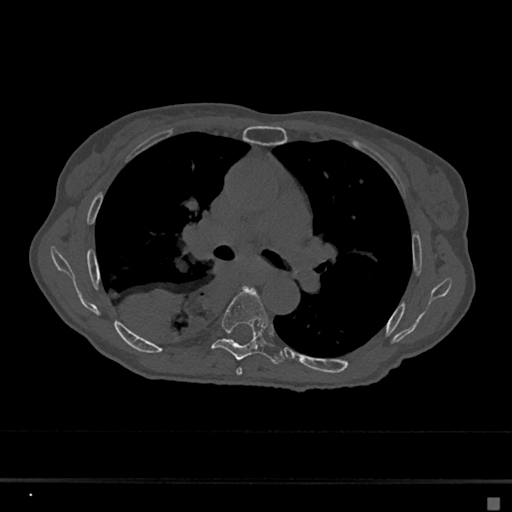
CT including the spine, one axial slice. Position 422 of 797 along the scan axis. Reconstruction kernel Br40s/3. 120 kVp. Bone window (W 1800 / L 400 HU). 512 × 512 image matrix, field of view 360 × 360 mm. Female patient, age 68 years. From the clinical record (not read from this slice): primary cancer: renal.
Outlined on this slice (semi-automatically segmented with operator editing):
- T5 vertebra: bounding box [x1, y1, x2, y2] px = [236, 287, 256, 375]
- T6 vertebra: [211, 286, 284, 364]